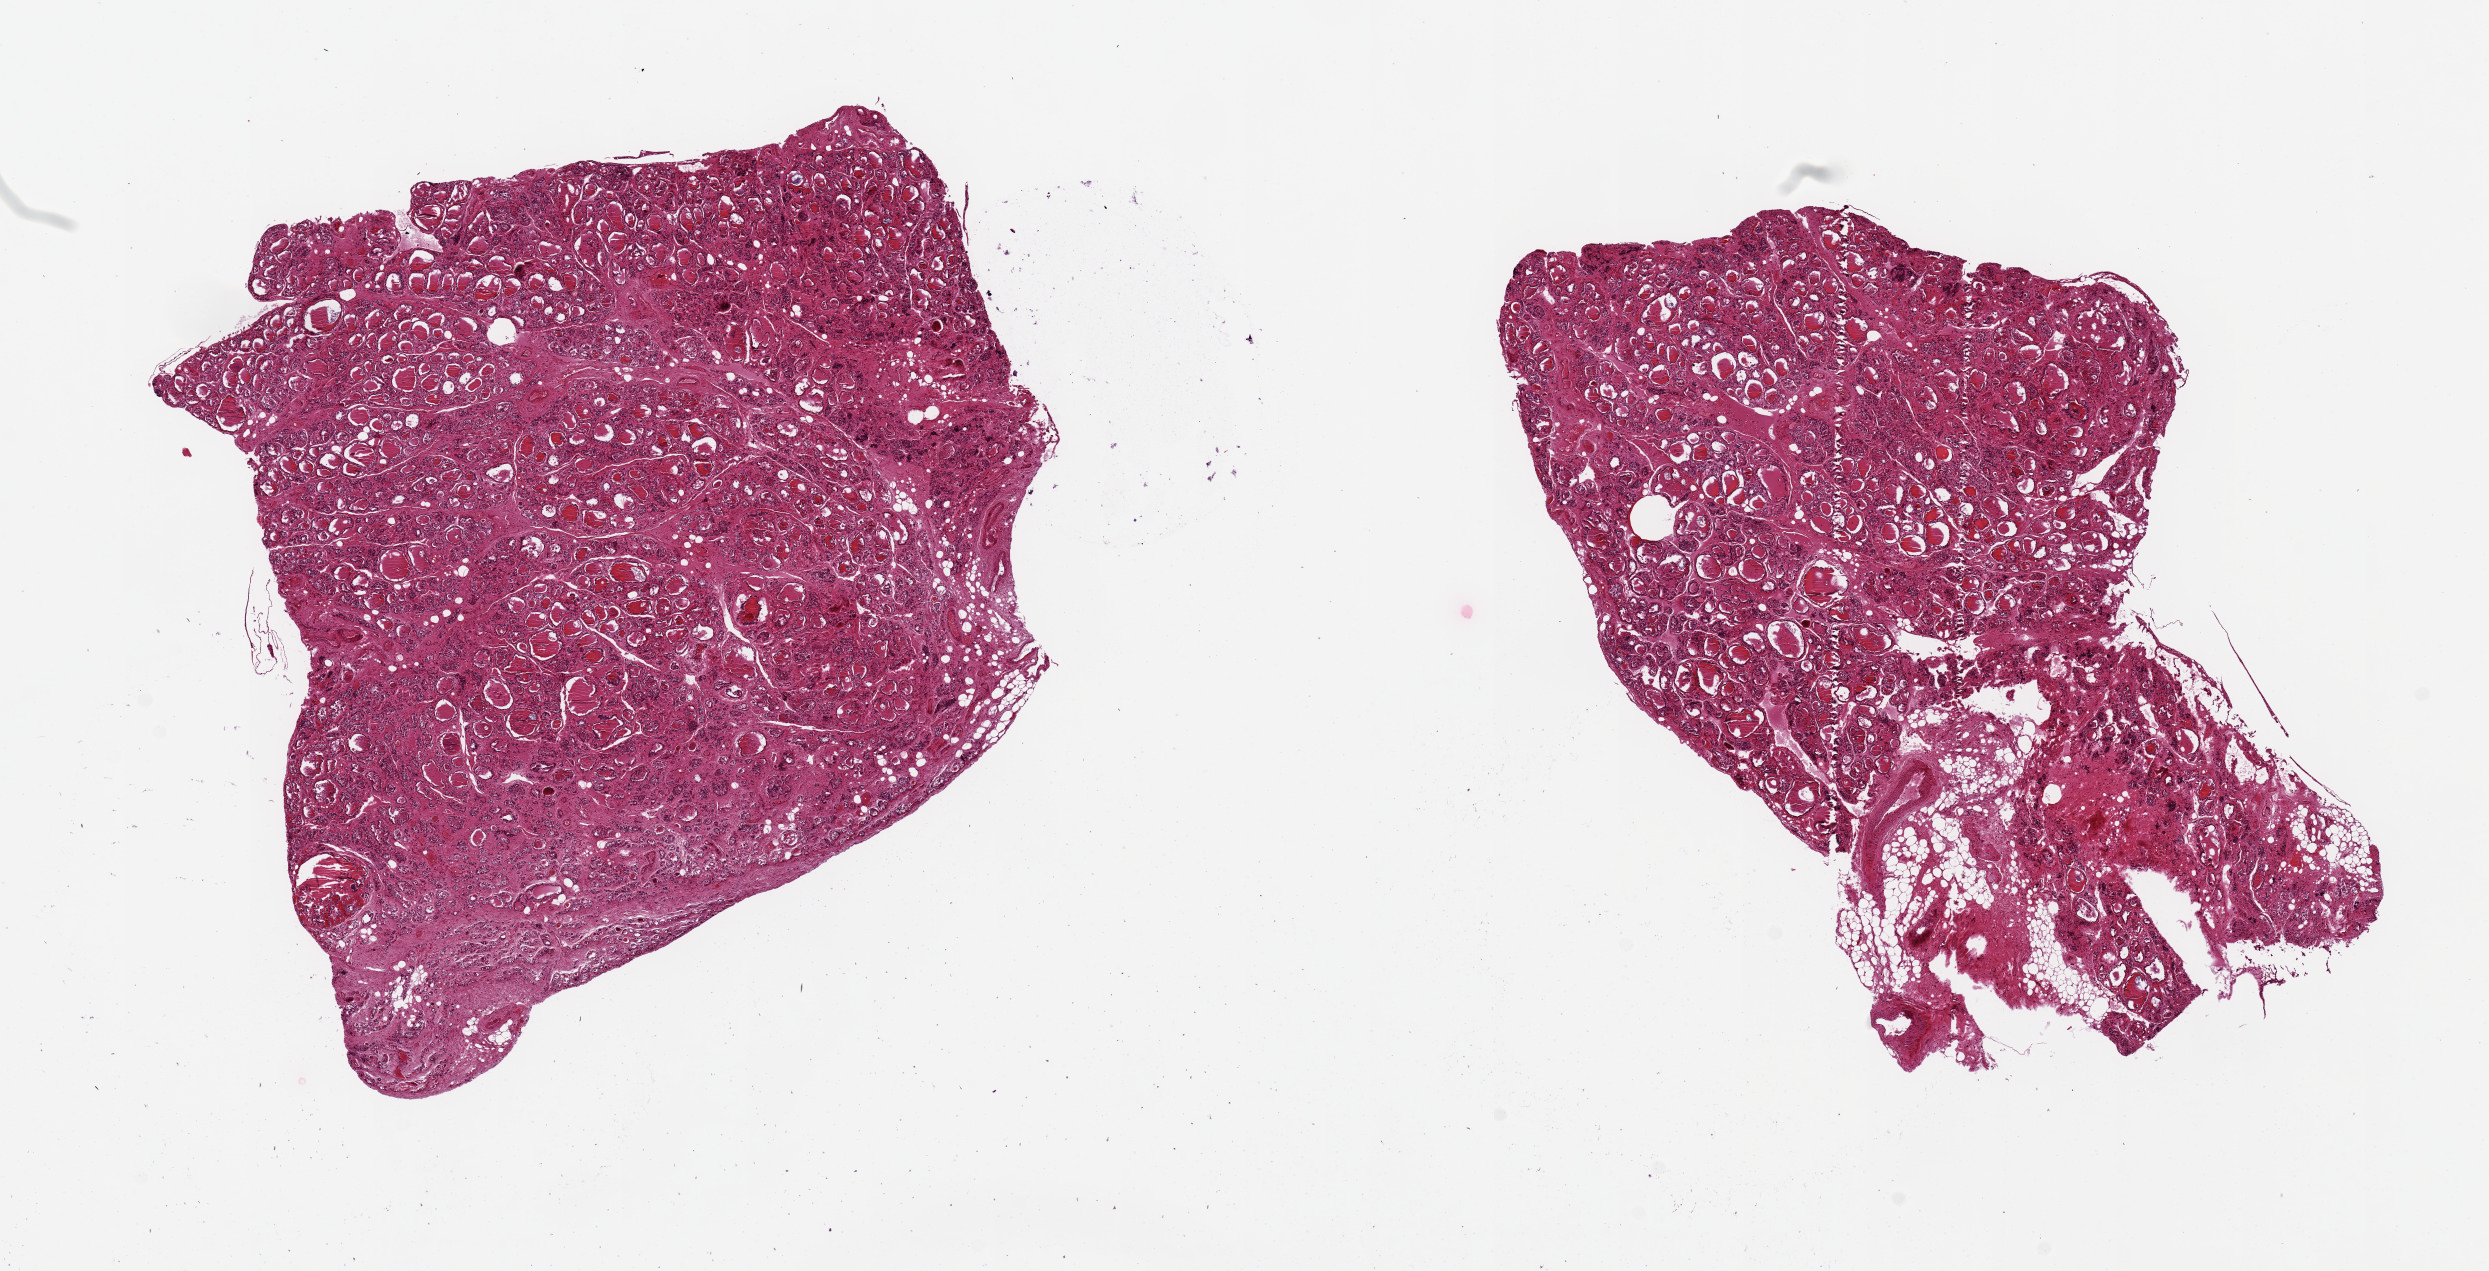
Whole-slide image, H&E stain — low-resolution overview of the scanned area, about 19.7 x 10.1 mm (from a 20x scan). PAXgene-fixed, paraffin-embedded tissue. Target tissue: thyroid. Tissue donor sample. Female donor.
* reviewer comment on this tissue sample: pieces, 8x5 & 7x6mm; ~20% adipose around one piece